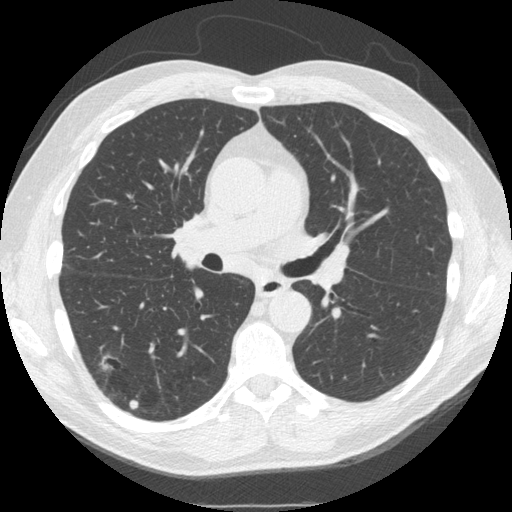
Low-dose screening chest CT, one axial slice; slice 93 of 162 in the series (ordered by position); lung window (W 1500 / L -600 HU); 2.5 mm slice thickness; 512 × 512 image matrix, field of view 360 × 360 mm.
Structures marked on this image (manually delineated by an expert):
- lesion 1 (nodule, lower lobe of right lung): bounding box [x1, y1, x2, y2] px = [101, 355, 117, 370]
- lesion 2 (tumor, lower lobe of right lung): [129, 399, 140, 410]